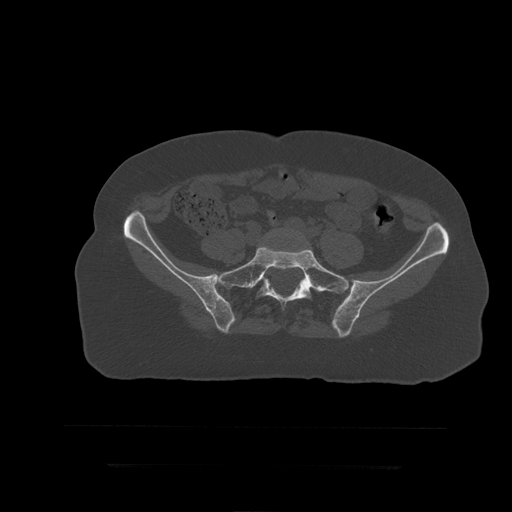
CT including the spine, one axial slice. Slice 54 of 399 in the series (ordered by position). Reconstruction kernel STANDARD. Bone window (W 1800 / L 400 HU). 512 × 512 image matrix, field of view 450 × 450 mm. Patient age 41 years. Case-level facts recorded for this patient, not image findings: primary cancer: breast.
Annotated regions visible in this slice (semi-automatically segmented with operator editing):
- L5 vertebra: box from (x=266, y=235) to (x=311, y=249) px